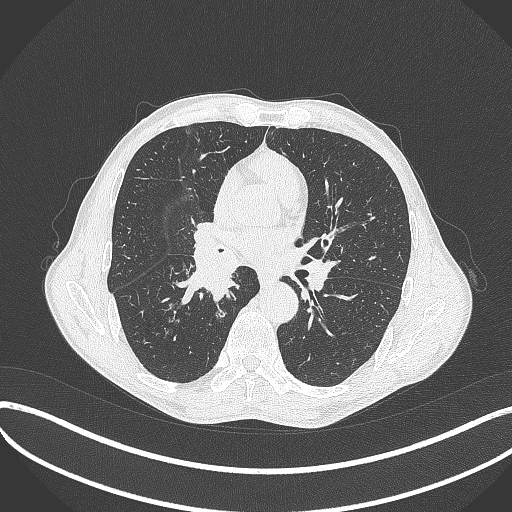
Chest CT, one axial slice. Slice 227 of 481 in the series (ordered by position). Reconstruction kernel B70f. 120 kVp. Lung window (W 1500 / L -600 HU). 512 × 512 image matrix. Patient: male, 65 years. Case-level facts recorded for this patient, not image findings: clinical TNM (as recorded): T2a N0 M0; histopathological grade: G2.
Outlined on this slice (rectangle marked by the reading radiologist):
- lung tumour (recorded histology: squamous cell carcinoma): bounding box [x1, y1, x2, y2] px = [182, 231, 239, 308]